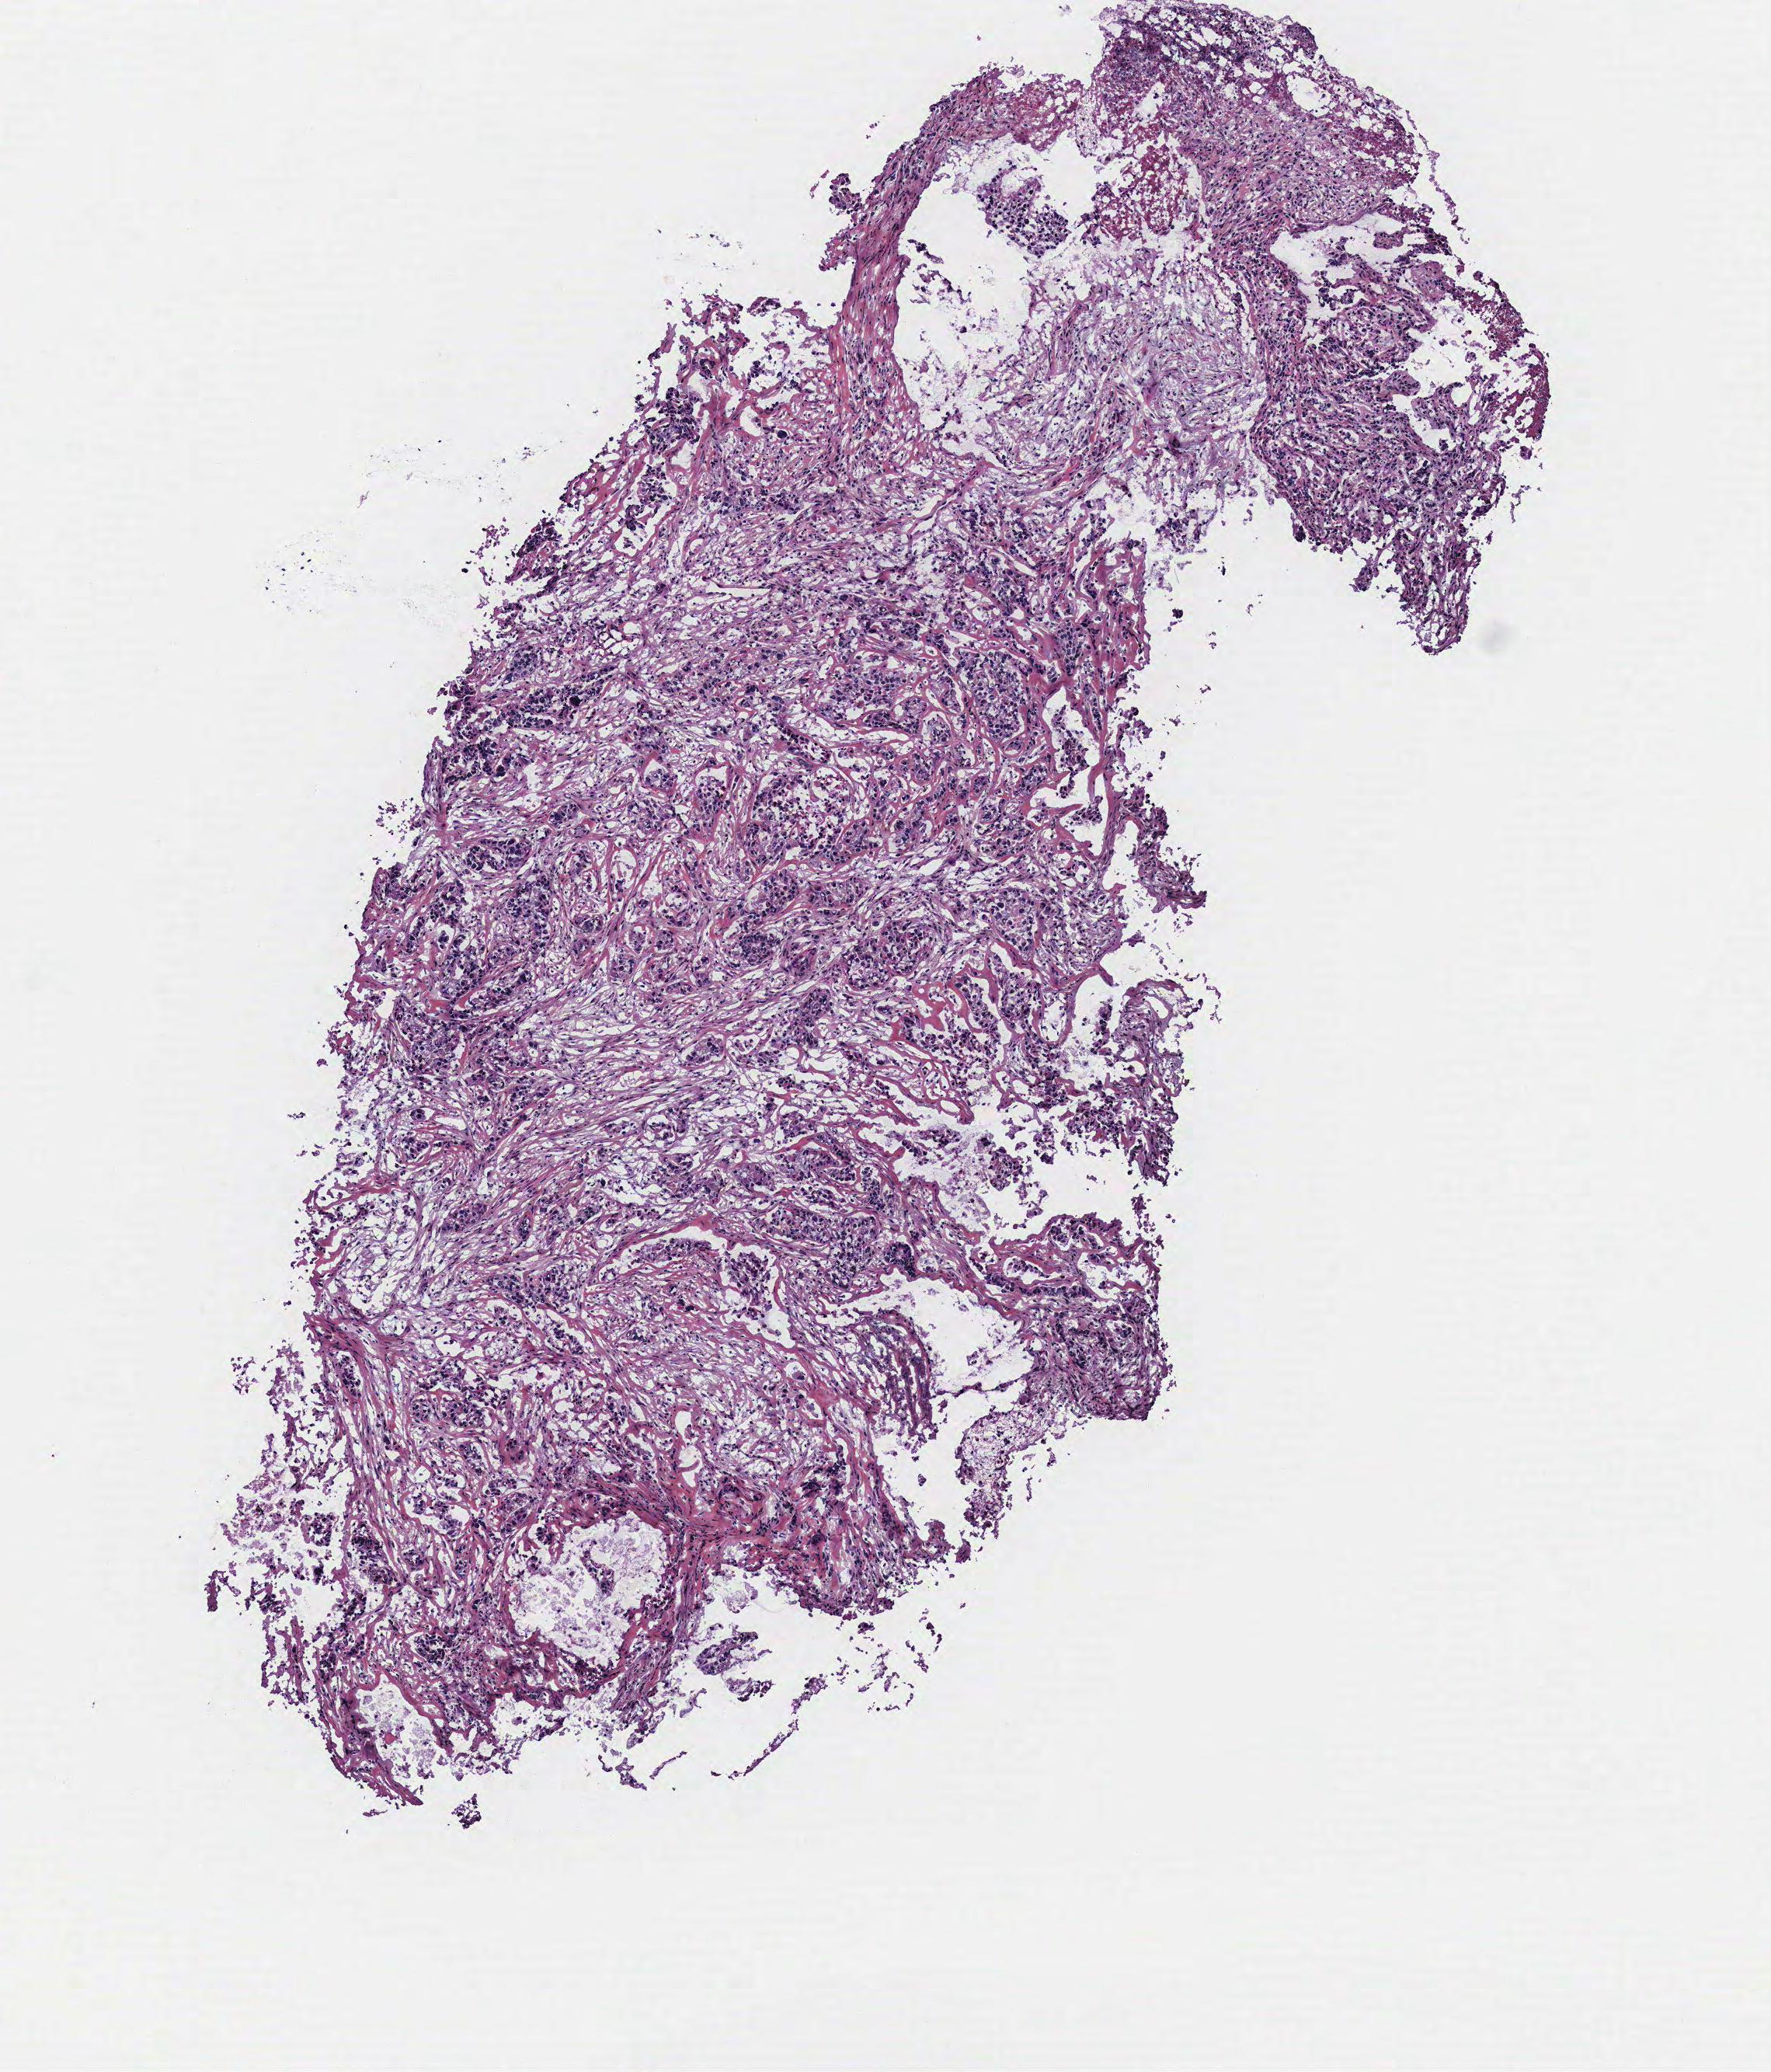
H&E-stained whole-slide image, whole scanned area (about 4.6 x 5.3 mm, slide scanned at 40x) shown as a low-resolution overview; tumour tissue sample, ovary. 55-year-old female patient.
• patient diagnosis (cohort enrolment): ovarian cancer (ovary)